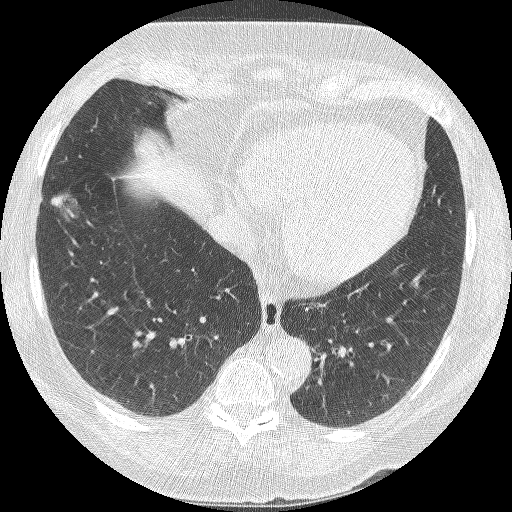
Low-dose screening chest CT, axial slice, second annual screen, lung window (W 1500 / L -600 HU), 1.25 mm slice thickness, lung (sharp) reconstruction kernel (BONE), slice 91 of 245 in the series. Female, age 68 years at enrolment.
Lesion marked by an expert reader, bounding box <35,191,83,244> (left, top, right, bottom; pixels). Reader record for this screening exam (exam-level; its link to the box is not recorded): non-calcified nodule or mass ≥4 mm, right lower lobe, 18 × 15 mm, poorly defined margins, ground glass attenuation, pre-existing on the prior screen: yes; interval growth: yes. Official screen result: positive, other.